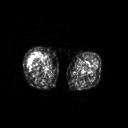
FDG PET of an extremity soft-tissue mass (from a PET/CT study), one axial slice; position 213 of 311 along the scan axis; 3.27 mm slice thickness; 128 × 128 image matrix, field of view 500 × 500 mm. Patient: female, 57 years. Case-level facts recorded for this patient, not image findings: histological type: pleiomorphic undifferentiated sarcoma; grade: high; site of the primary tumour: right quadricep.
Annotated regions visible in this slice (expert contour drawn on MRI and transferred to this co-registered scan by the dataset authors):
- tumour plus oedema (research contour): box from (x=27, y=52) to (x=41, y=66) px